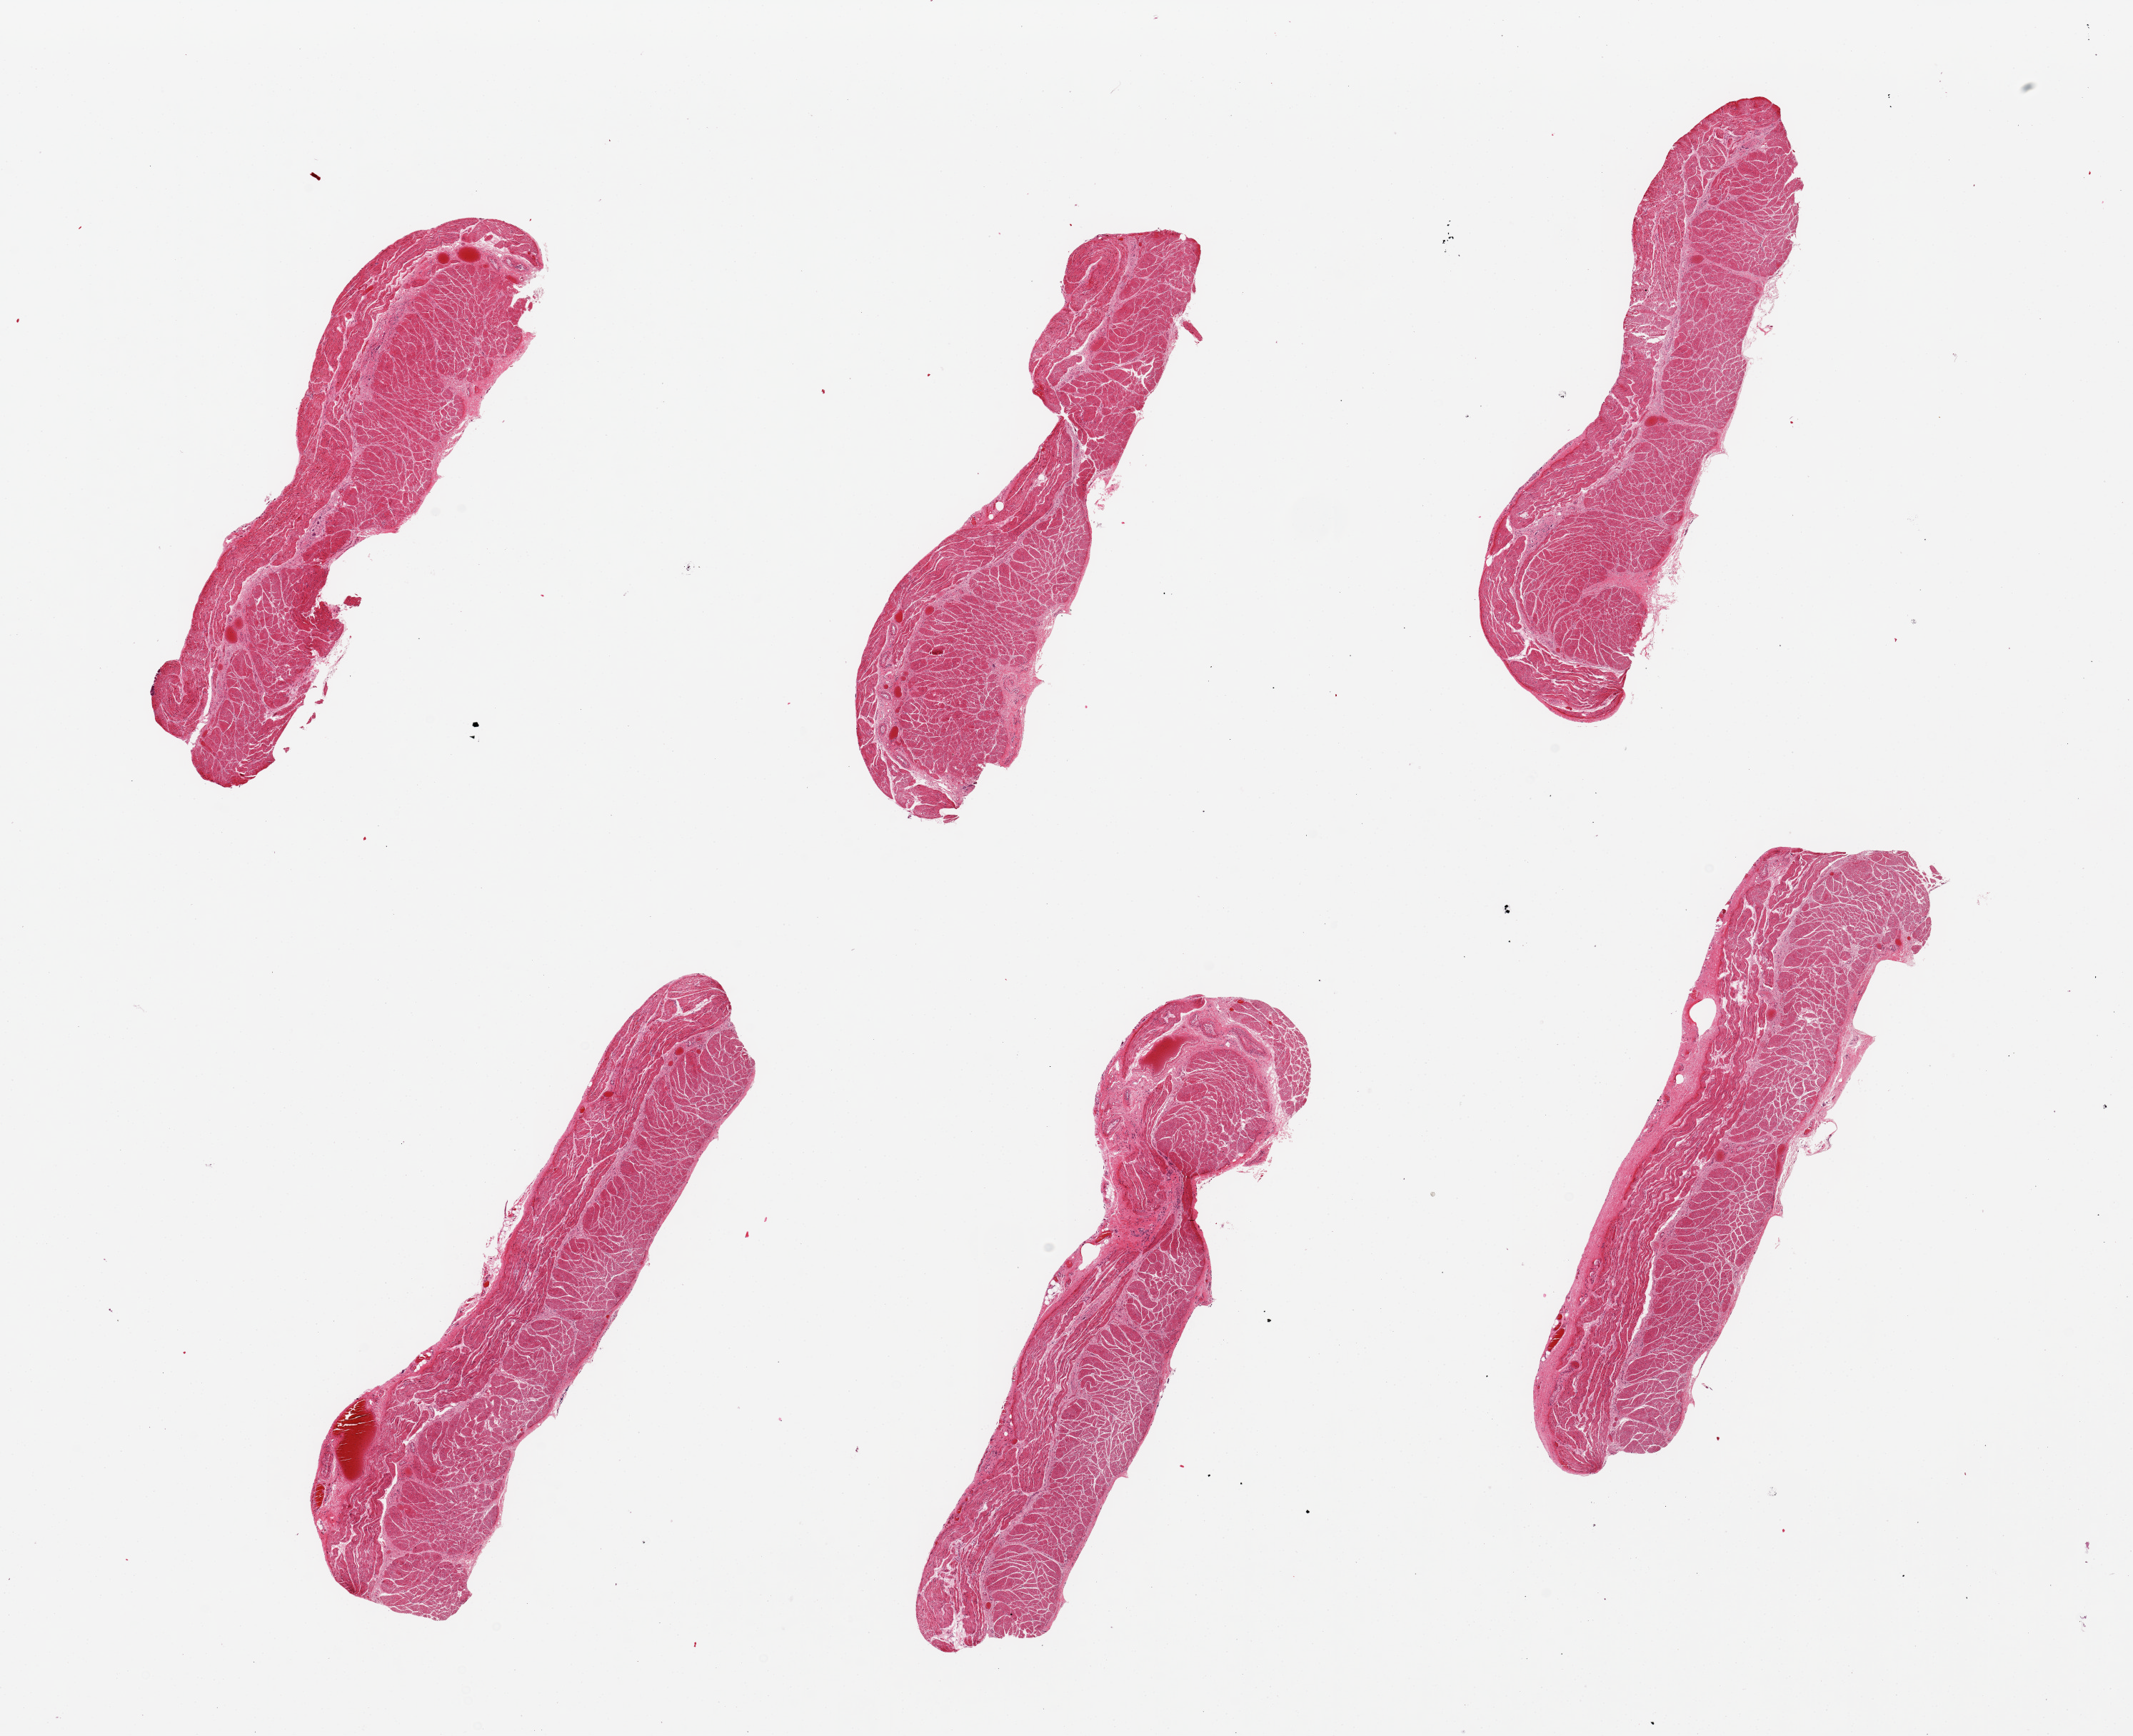
Whole-slide image, H&E stain, brightfield — shown as a low-resolution overview of the whole scanned area (about 23.6 x 19.2 mm); PAXgene-fixed paraffin-embedded (PFPE) section; target tissue: esophageal muscle; donor tissue sample. Donor sex: male.
• pathologist's review note for this sample: 6 pieces; well trimmed